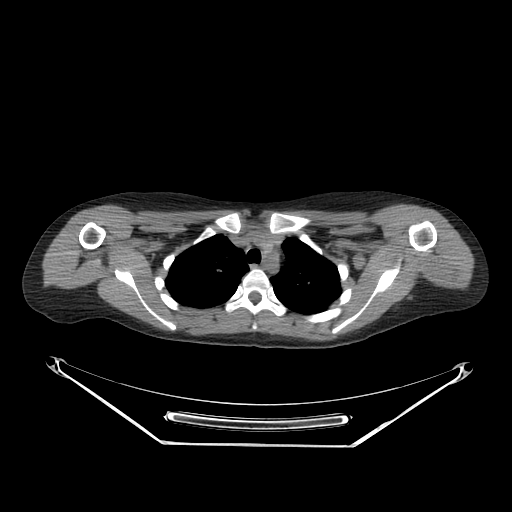
CT of an extremity soft-tissue mass (from a PET/CT study), one axial slice; slice 208 of 267 in the series (ordered by position); reconstruction kernel SOFT; 140 kVp; soft-tissue window (W 400 / L 40 HU); 3.75 mm slice thickness; 512 × 512 image matrix, field of view 500 × 500 mm. Female patient. Case-level facts recorded for this patient, not image findings: histological type: malignant fibrous histiocytoma; grade: low; site of the primary tumour: left arm.
Outlined on this slice (expert contour drawn on MRI and transferred to this co-registered scan by the dataset authors):
- gross tumour volume (mass): bounding box (x1, y1, x2, y2) in pixels: (422, 251, 458, 284)